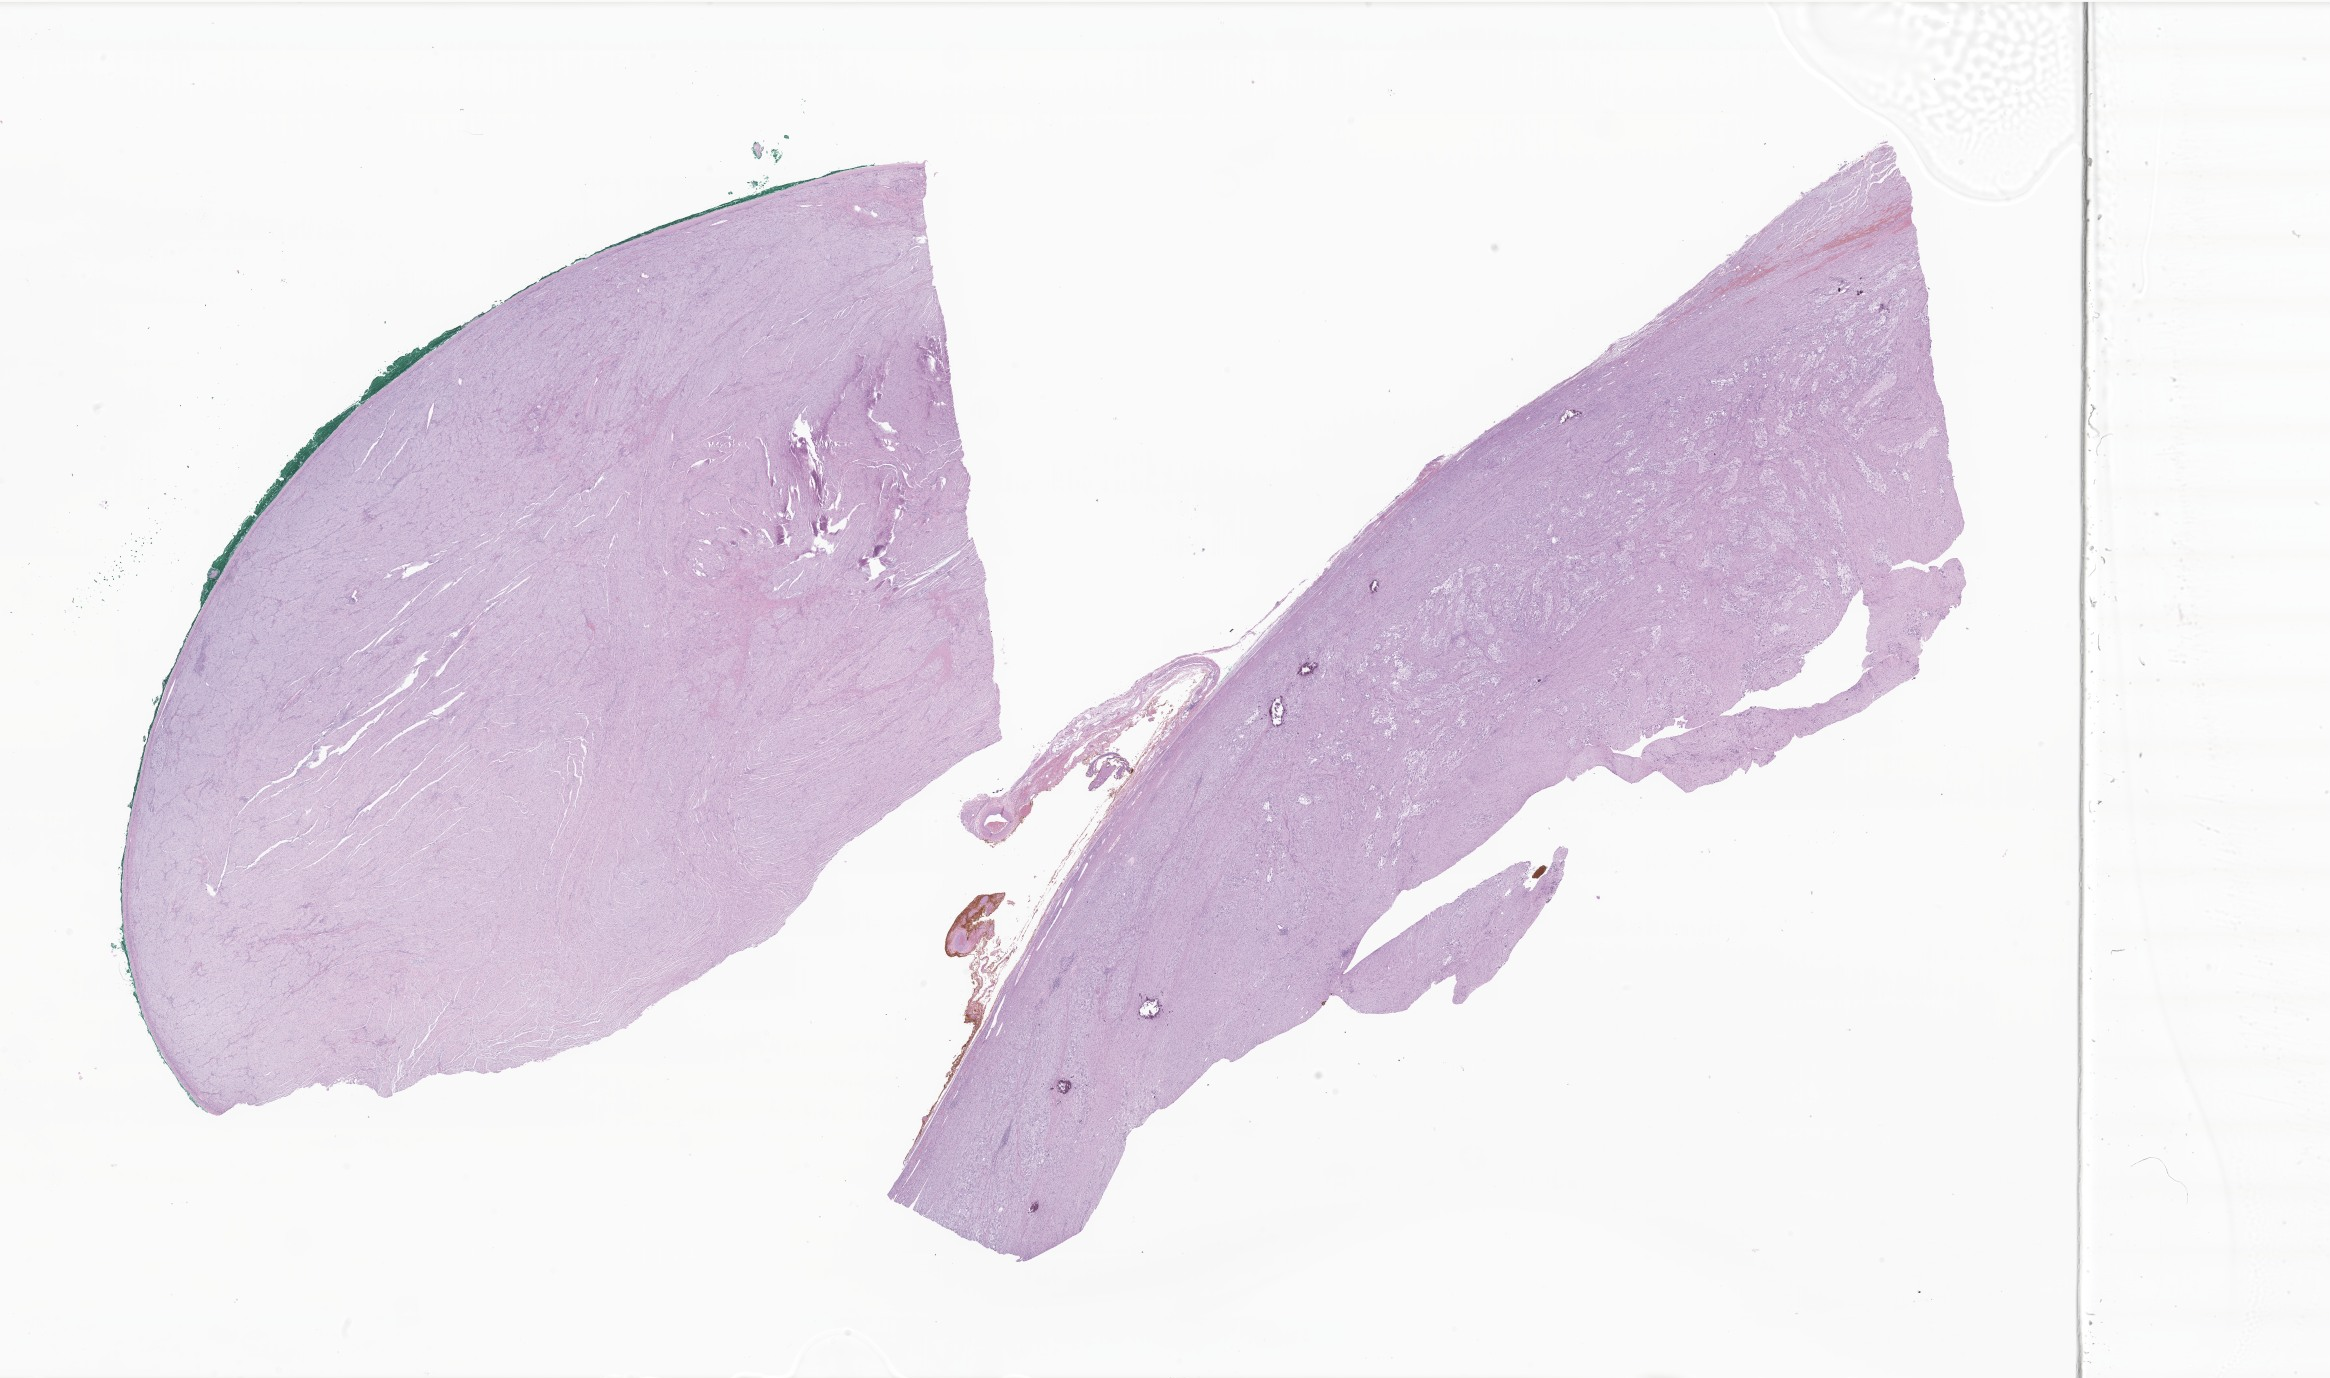
Whole-slide image, H&E stain of tumor tissue from the retroperitoneum — low-resolution overview of the scanned area, about 39.3 x 23.2 mm, FFPE section. Patient: male, age 100 months (8 years 4 months).
• recorded diagnosis: Ganglioneuroblastoma